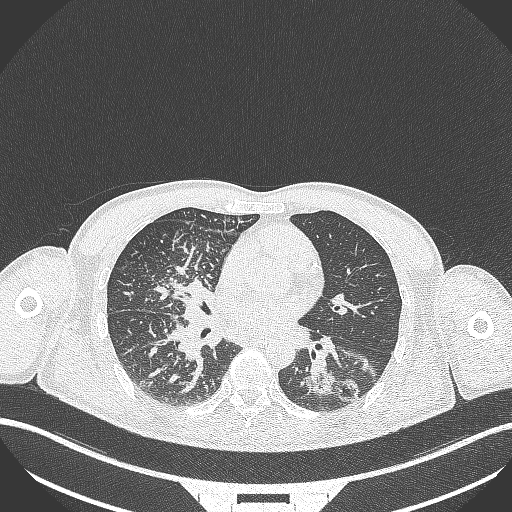
Chest CT, one axial slice. Slice 154 of 348 in the series (ordered by position). Reconstruction kernel B70f. 120 kVp. Lung window (W 1500 / L -600 HU). 1 mm slice thickness. 512 × 512 image matrix, field of view 400 × 400 mm. Male patient, age 49 years. From the clinical record (not read from this slice): clinical TNM (as recorded): T2b N1 M0.
Annotated regions visible in this slice (rectangle marked by the reading radiologist):
- lung tumour (recorded histology: adenocarcinoma): bounding box (x1, y1, x2, y2) in pixels: (306, 361, 365, 410)